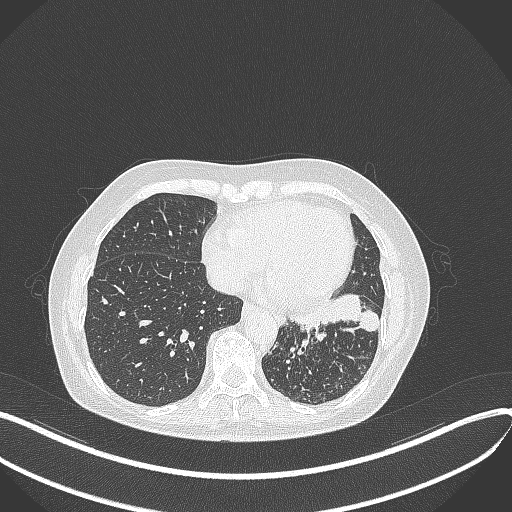
Chest CT, one axial slice; slice 137 of 429 in the series (ordered by position); lung window (W 1500 / L -600 HU); 512 × 512 image matrix, field of view 400 × 400 mm. Patient: female, 63 years. Case-level facts recorded for this patient, not image findings: clinical TNM (as recorded): T1b N0 M0; histopathological grade: G2-3.
Structures marked on this image (rectangle marked by the reading radiologist):
- lung tumour (recorded histology: adenocarcinoma): bounding box (x1, y1, x2, y2) in pixels: (286, 289, 381, 341)